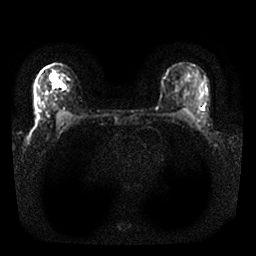
Breast MRI, one axial slice. Diffusion-weighted series; image 2 of 4 stored at this slice position (different b-values; order by instance number). 1.5 T. 256 × 256 image matrix, field of view 310 × 310 mm. Female patient.
Outlined on this slice (expert manual segmentation):
- tumour on diffusion-weighted imaging: bounding box <49,75,56,82> (left, top, right, bottom; pixels)